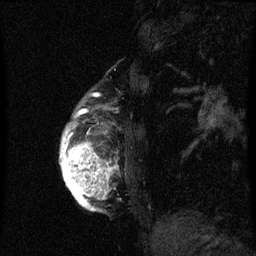
Breast MRI (dynamic contrast-enhanced), one sagittal slice. Position 10 of 60 along the scan axis. Dynamic contrast-enhanced series, image 2 of 3 at this slice position (ordered by acquisition). 1.5 T. TE 4.2 ms, TR 8 ms. 256 × 256 image matrix, field of view 180 × 180 mm. Female patient, age 56 years.
Outlined on this slice (semi-automatic segmentation, software-assisted and operator-edited):
- analysis volume of interest (the breast-tissue region the enhancement analysis was run in; not a lesion): bounding box [x1, y1, x2, y2] px = [60, 96, 121, 213]
- tumour enhancement mask (voxels above the 70 % enhancement threshold inside the analysis volume of interest): [60, 110, 113, 211]